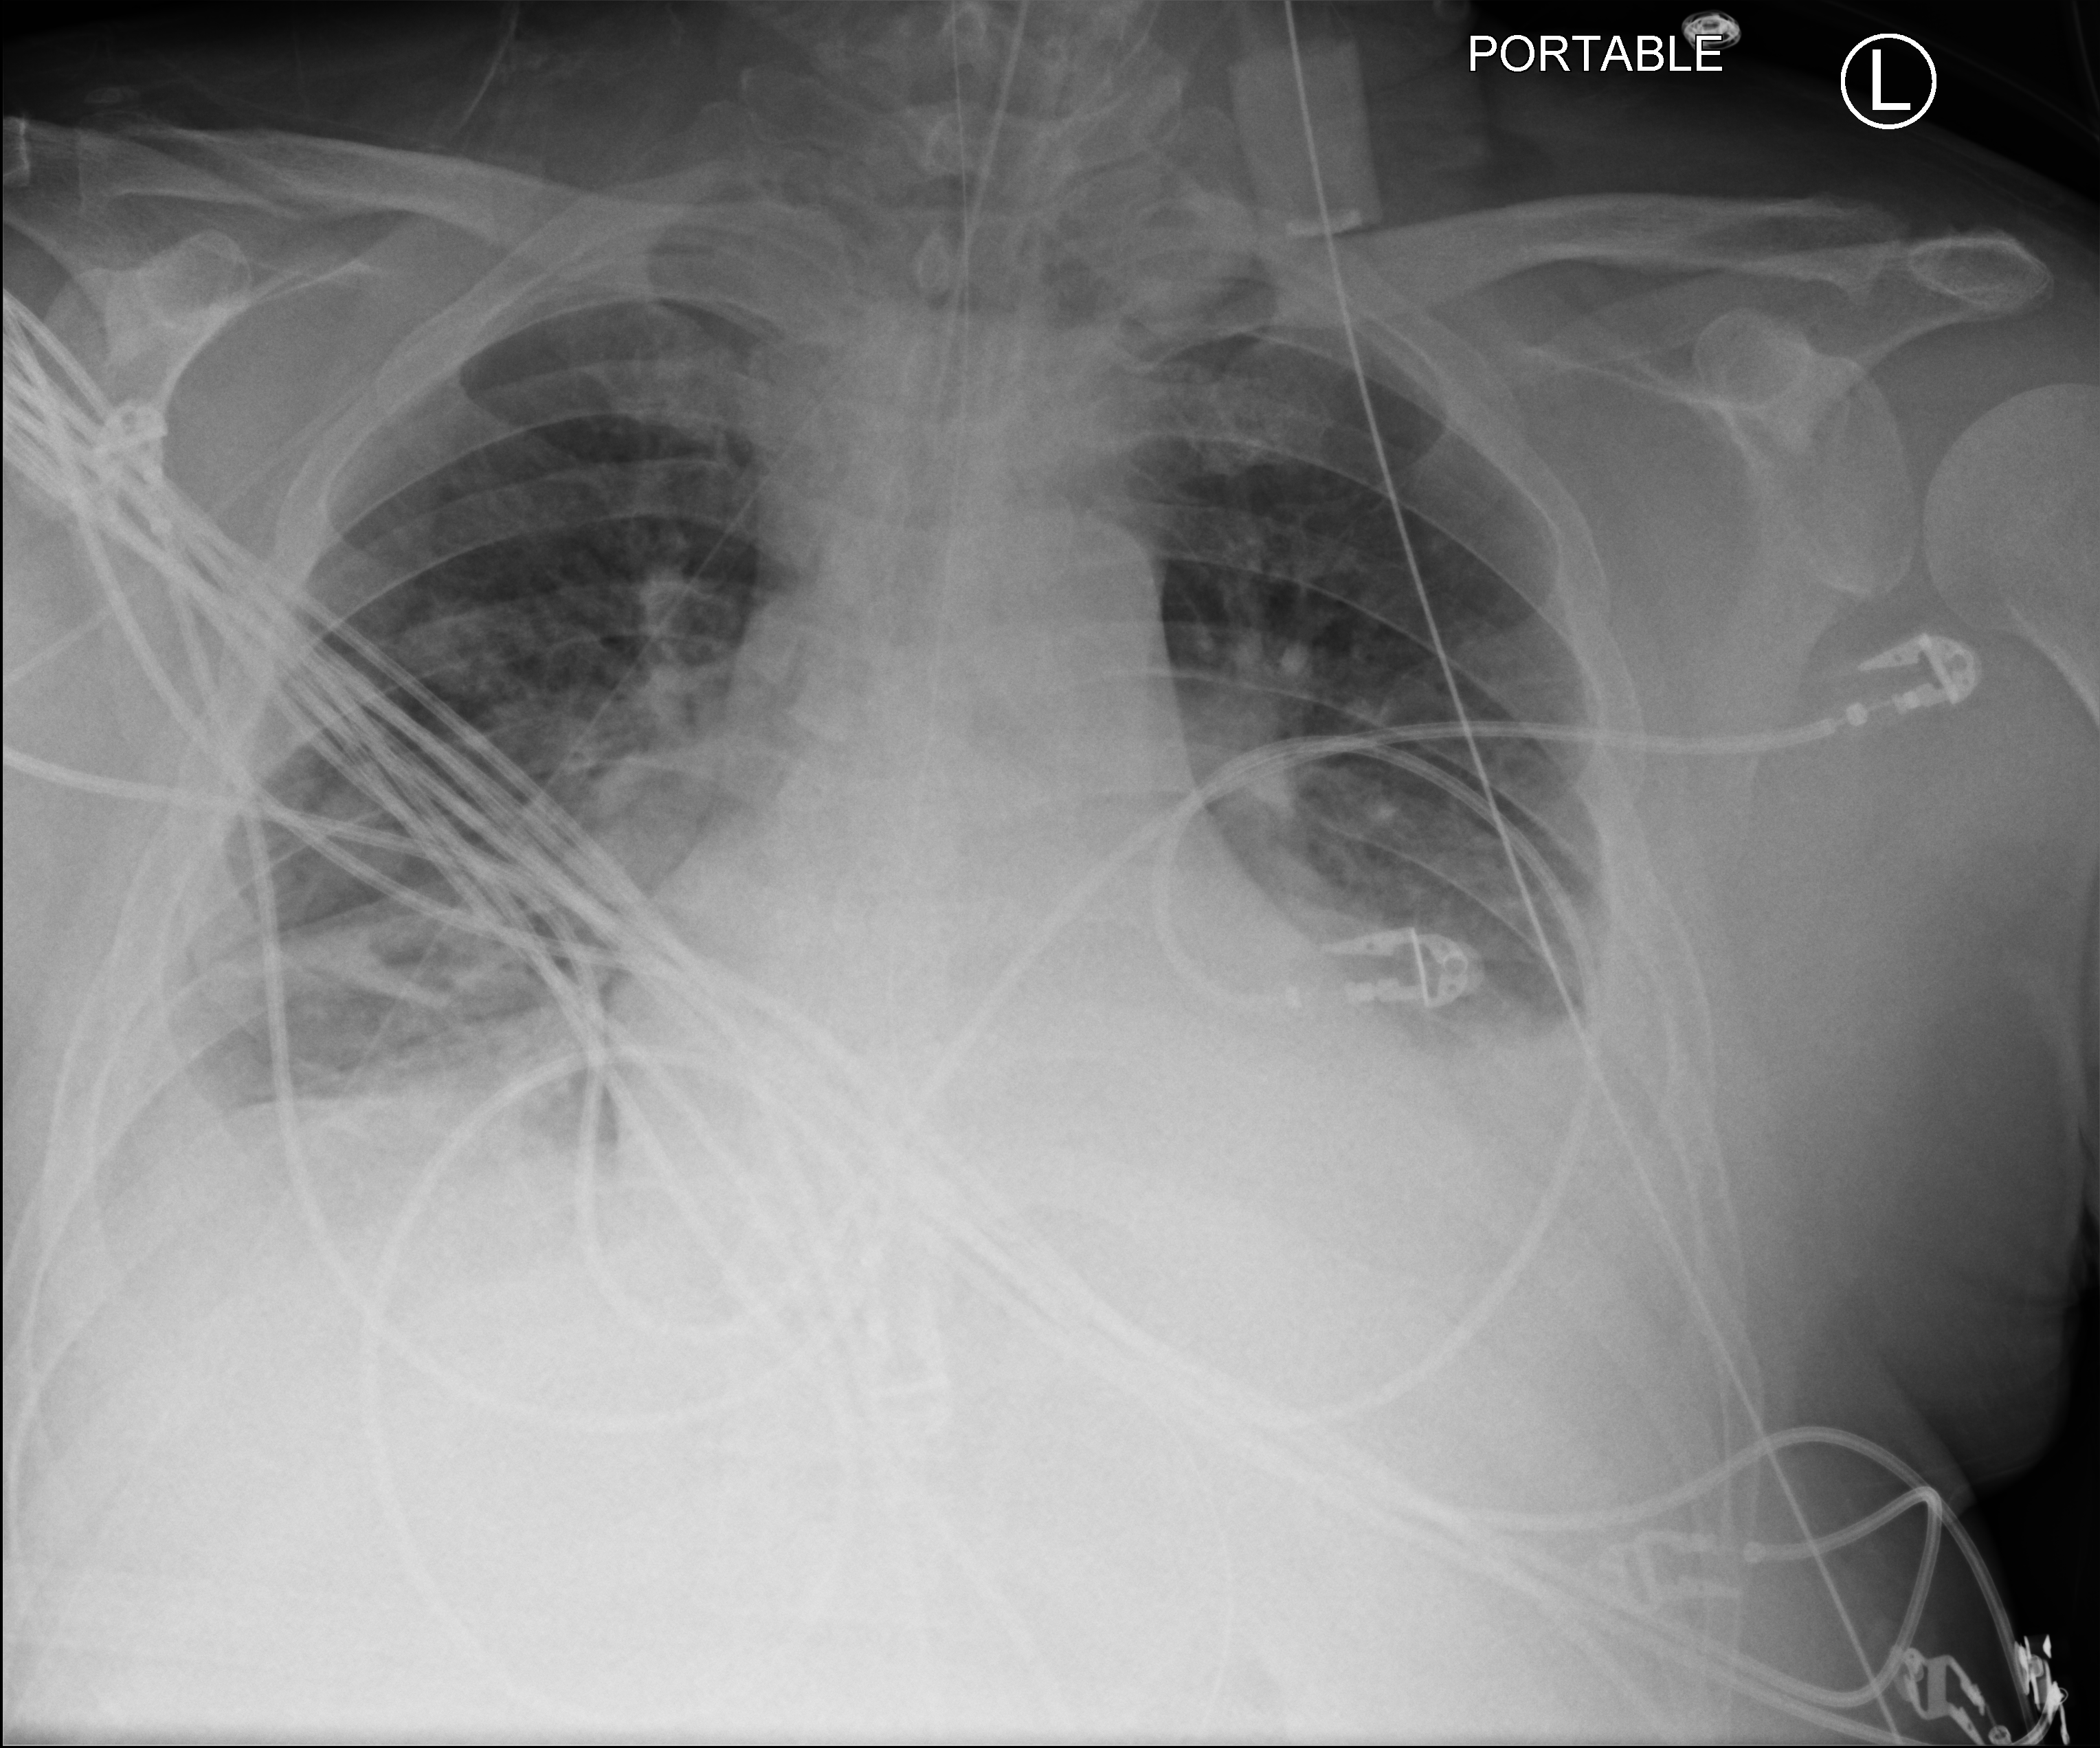
Chest X-ray (portable), anteroposterior (AP) projection. Patient hospitalised with COVID-19; male, aged 18–59 years.
From the hospital-stay record, not from the radiograph (when in the stay this image was taken is not recorded): admitted to intensive care during this hospital stay: yes.